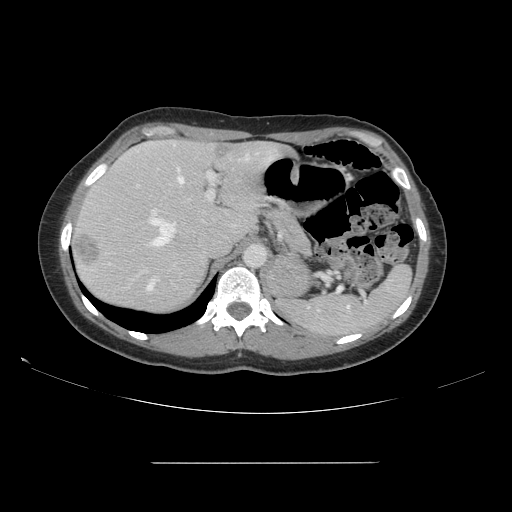
Contrast-enhanced abdominal CT, one axial slice. Position 111 of 151 along the scan axis. 120 kVp. Intravenous contrast given. Soft-tissue window (W 400 / L 40 HU). 2.5 mm slice thickness. 512 × 512 image matrix, field of view 421 × 421 mm. Female patient, age 46 years. From the clinical record (not read from this slice): diagnosis: colorectal cancer liver metastases, imaged before liver resection; multiple liver metastases: yes; largest metastasis: 3 cm; disease in both lobes: yes.
Annotated regions visible in this slice (expert manual segmentation):
- hepatic veins: box from (x=149, y=153) to (x=251, y=247) px
- liver: (x=71, y=140)–(x=288, y=313)
- planned liver remnant (the part of the liver to remain after resection): (x=88, y=140)–(x=289, y=252)
- portal vein (with intrahepatic branches): (x=137, y=172)–(x=215, y=291)
- liver metastasis: (x=75, y=232)–(x=102, y=266)
- liver metastasis: (x=213, y=145)–(x=229, y=160)